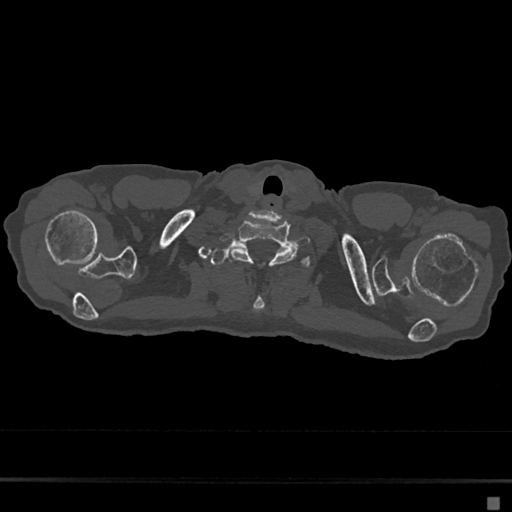
CT including the spine, one axial slice; position 630 of 797 along the scan axis; reconstruction kernel Br40s/3; bone window (W 1800 / L 400 HU); 512 × 512 image matrix, field of view 360 × 360 mm. Patient: female, 68 years. Case-level facts recorded for this patient, not image findings: primary cancer: renal.
Outlined on this slice (semi-automatic segmentation, software-assisted and operator-edited):
- T1 vertebra: bounding box (x1, y1, x2, y2) in pixels: (210, 243, 311, 312)